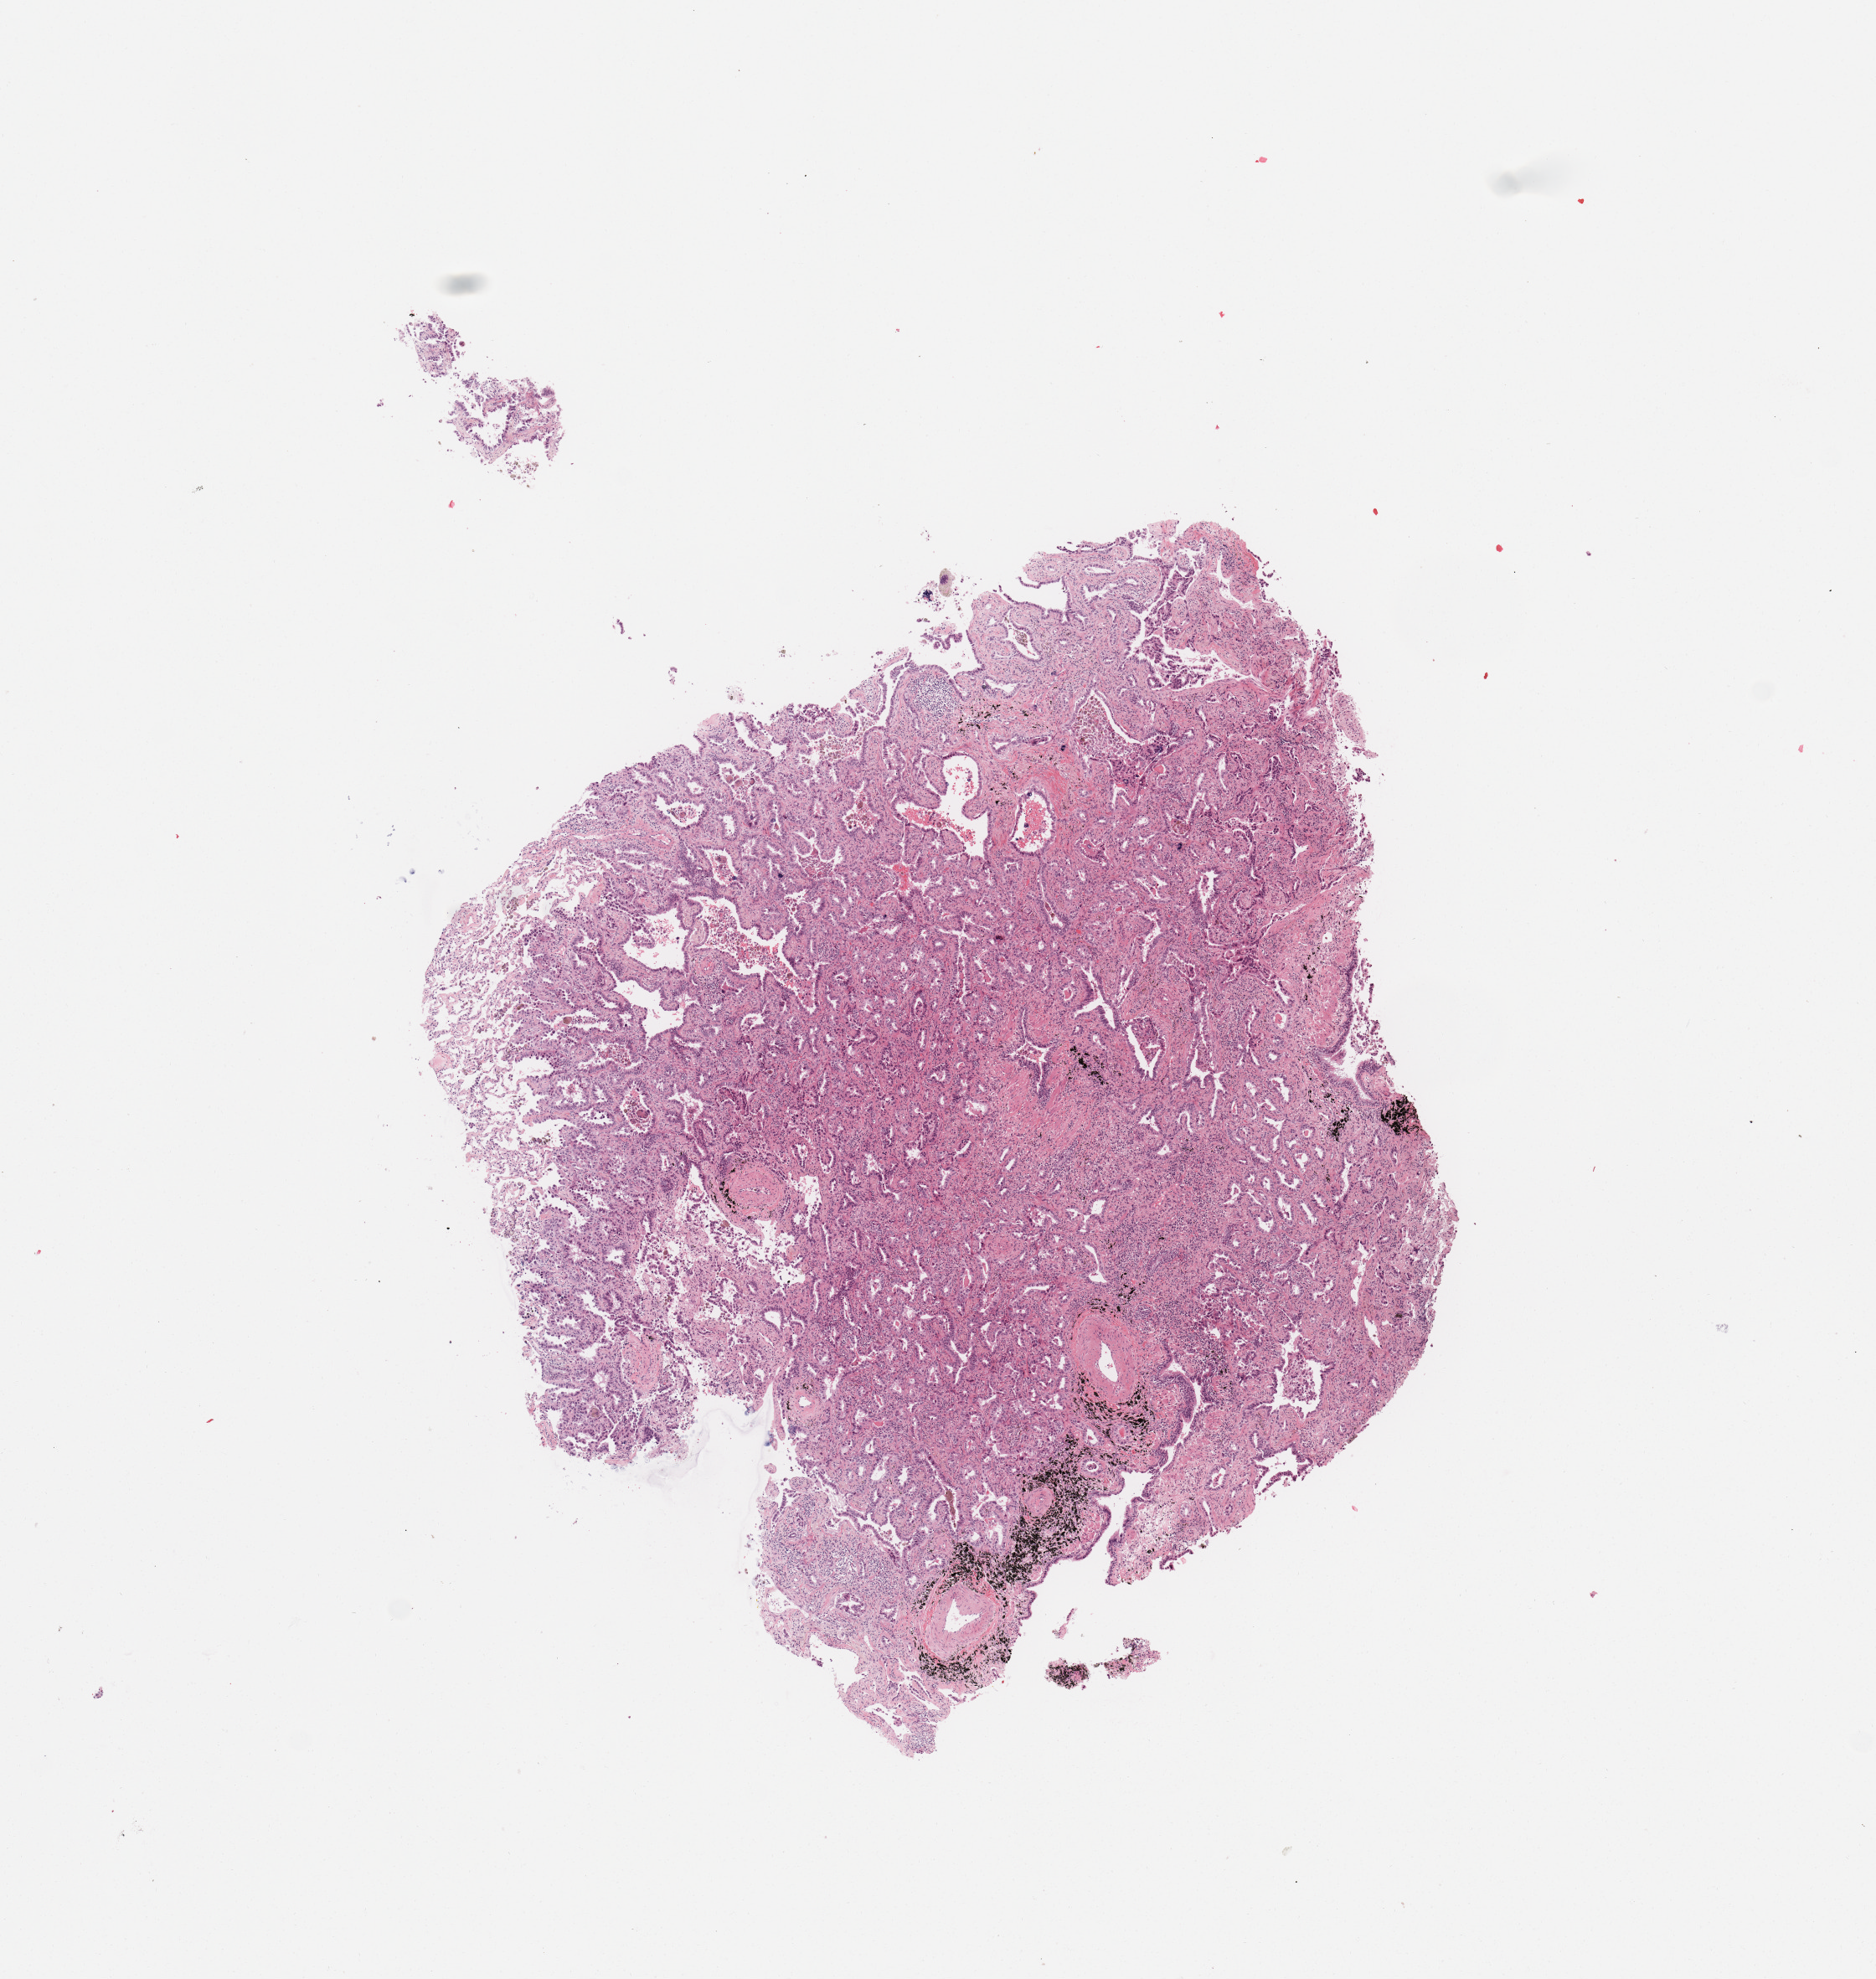
Digitized Hematoxylin and eosin (H&E) stained tissue section (whole slide), whole scanned area (about 8.9 x 9.3 mm, slide scanned at 20x) shown as a low-resolution overview; tumour tissue sample, sampled site: lung. Patient: male, age 72 years. Histologic grade: G2 (moderately differentiated). Composition of this section per pathologist review: tumour nuclei 70%, necrosis 0%.
- AJCC pathologic stage: IA3
- diagnosis: Adenocarcinoma, NOS